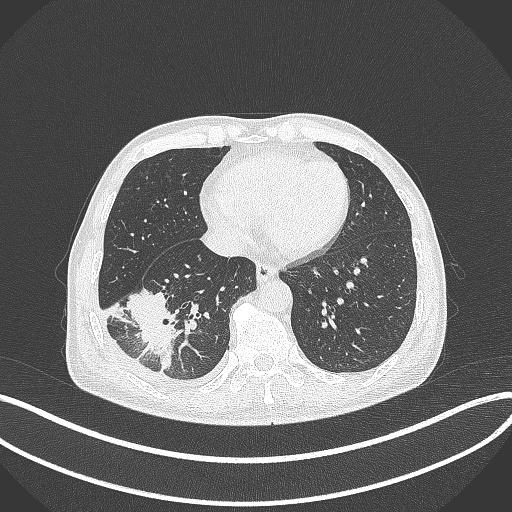
Chest CT, one axial slice. Slice 121 of 388 in the series (ordered by position). Reconstruction kernel B70f. Lung window (W 1500 / L -600 HU). 1 mm slice thickness. 512 × 512 image matrix. Patient: male, 64 years. Case-level facts recorded for this patient, not image findings: clinical TNM (as recorded): T3 N0 M0; histopathological grade: G2-3.
Structures marked on this image (bounding box drawn by a radiologist):
- lung tumour (recorded histology: adenocarcinoma): bounding box [x1, y1, x2, y2] px = [123, 285, 180, 372]